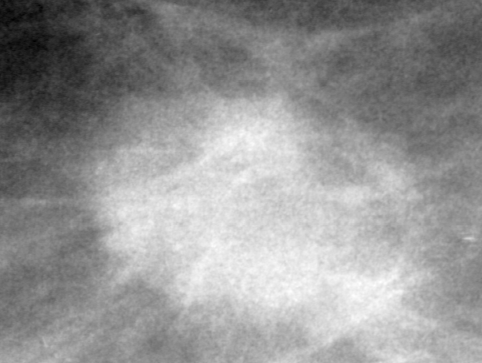
Cropped region of a digitized screen-film mammogram centred on a radiologist-marked abnormality, left breast, CC view, BI-RADS breast density category 2 (scale 1–4).
Marked abnormality: mass, shape irregular, margins spiculated; BI-RADS assessment category 5; pathology (as recorded): malignant.